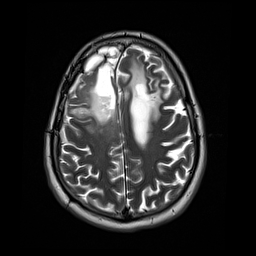
Brain MRI from a brain-tumour surgery series, one axial slice. Position 13 of 44 along the scan axis. 4 mm slice thickness. 256 × 256 image matrix, field of view 240 × 240 mm. Case-level facts recorded for this patient, not image findings: histopathology: Astrocytoma; WHO grade: 4; IDH mutation: yes.
Annotated regions visible in this slice (expert manual segmentation):
- tumour: bounding box (x1, y1, x2, y2) in pixels: (68, 90, 112, 134)